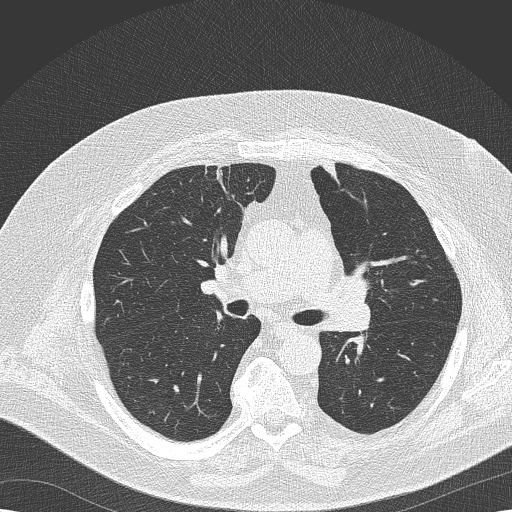
Chest CT (low-dose screening protocol), one axial image, second screening round (one year after baseline), lung window (W 1500 / L -600 HU), 2 mm slice thickness, 120 kVp, slice 73 of 173 in the series, 512 × 512 image matrix. Male participant, aged 68 years at enrolment. Former smoker at enrolment.
Lesion marked by an expert reader, bounding box [x1, y1, x2, y2] px = [320, 262, 385, 323]. Screening reader's record for this exam (one nodule recorded; not confirmed to be the boxed lesion): non-calcified nodule or mass ≥4 mm, left lower lobe, 8 × 6 mm, soft tissue attenuation, pre-existing on the prior screen: yes; interval growth: no. Official screen result: positive, no significant change: stable abnormalities potentially related to lung cancer, unchanged since the prior screening exam. Participant outcome: lung cancer diagnosed 256 days after this screen — squamous cell carcinoma, NOS, left upper lobe, poorly differentiated (G3), stage IIB (AJCC 6th edition), 35 mm at pathology.